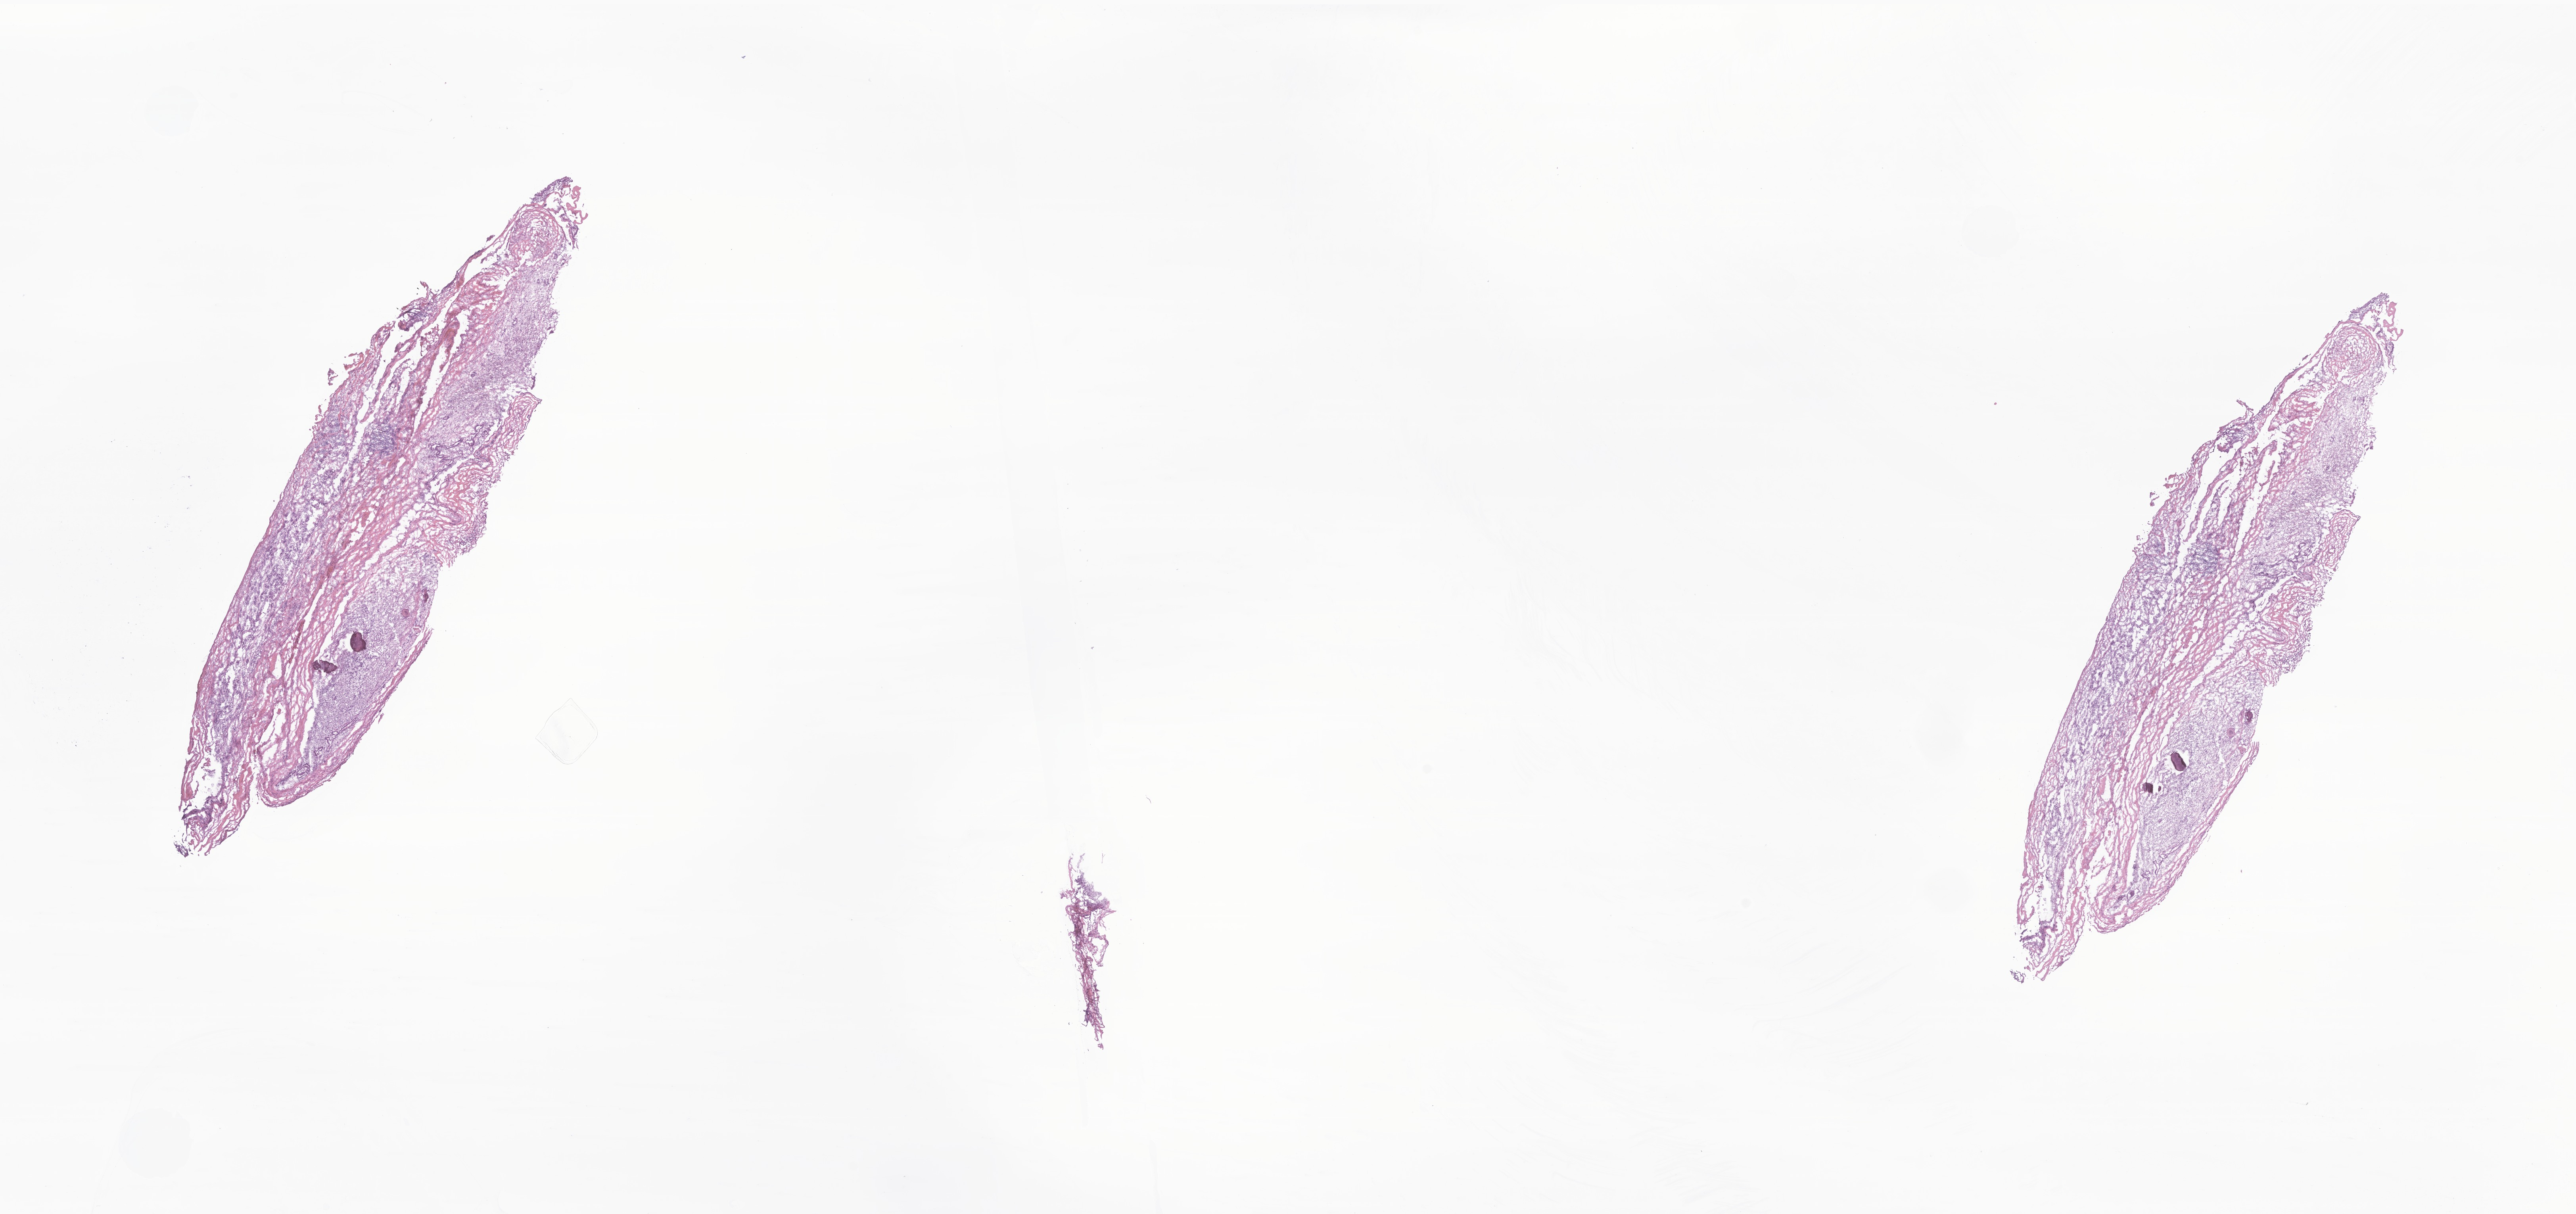
Whole-slide image, hematoxylin and eosin (H&E) stain of tumor tissue from the brain, whole scanned area (about 27.4 x 12.9 mm) shown as a low-resolution overview; frozen section. Patient: male, age 91 months (7 years 7 months).
Diagnosis (ICD-O-3 morphology term): Craniopharyngioma, adamantinomatous.